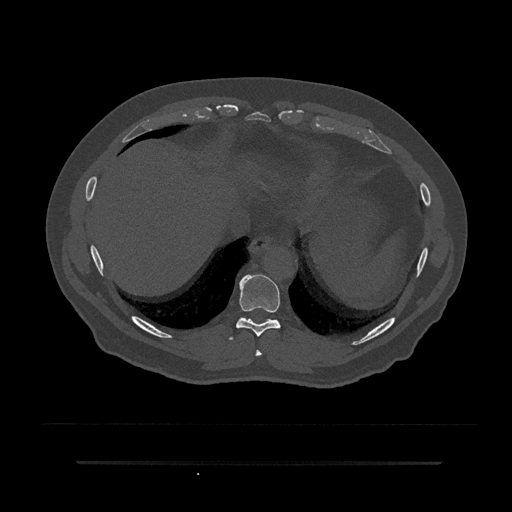
CT including the spine, one axial slice. Slice 371 of 797 in the series (ordered by position). Reconstruction kernel Br40s/3. Bone window (W 1800 / L 400 HU). 0.5 mm slice thickness. 512 × 512 image matrix, field of view 464 × 464 mm. Patient: male, 59 years. Case-level facts recorded for this patient, not image findings: primary cancer: bile ducts.
Structures marked on this image (semi-automatically segmented with operator editing):
- T8 vertebra: box from (x=255, y=349) to (x=262, y=357) px
- T9 vertebra: (x=229, y=274)–(x=281, y=340)